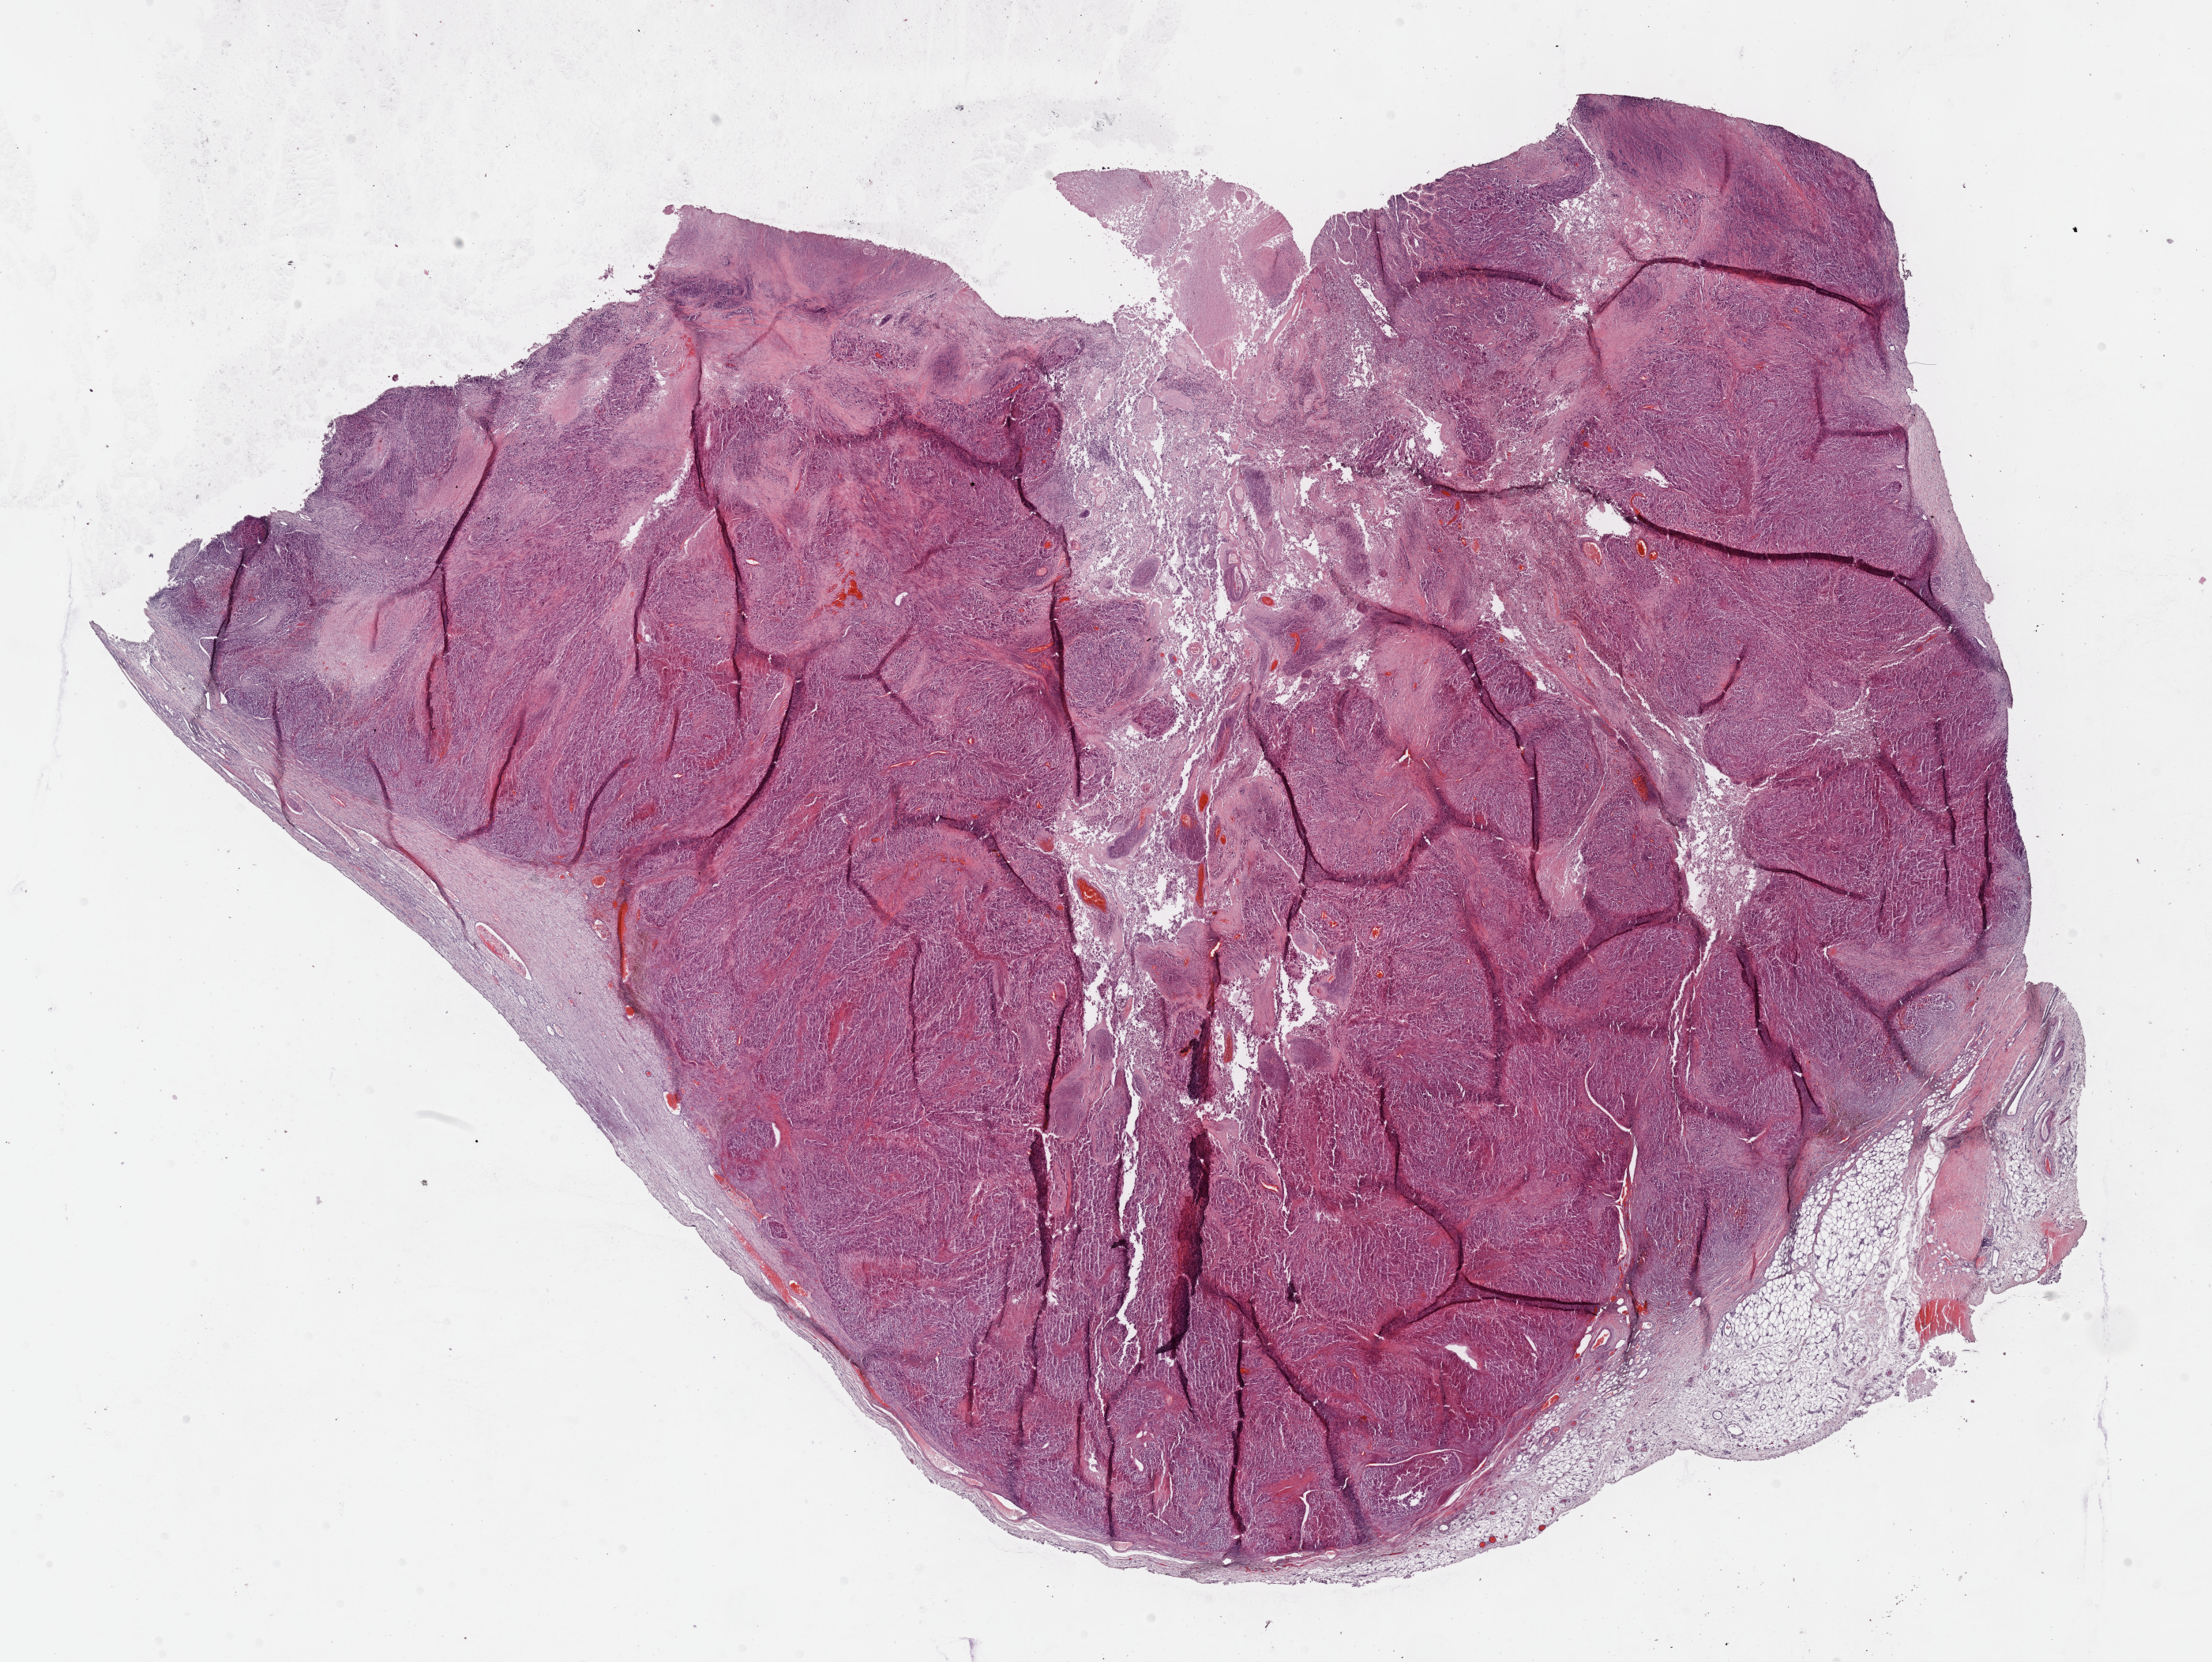
Digitized Hematoxylin and eosin (H&E) stained tissue section (whole slide) — shown as a low-resolution overview of the whole scanned area (about 22.7 x 17.0 mm). FFPE section. Primary tumour sample from the skin. Patient: male, age at initial diagnosis 63 years.
Pathologic diagnosis: Malignant melanoma, NOS.